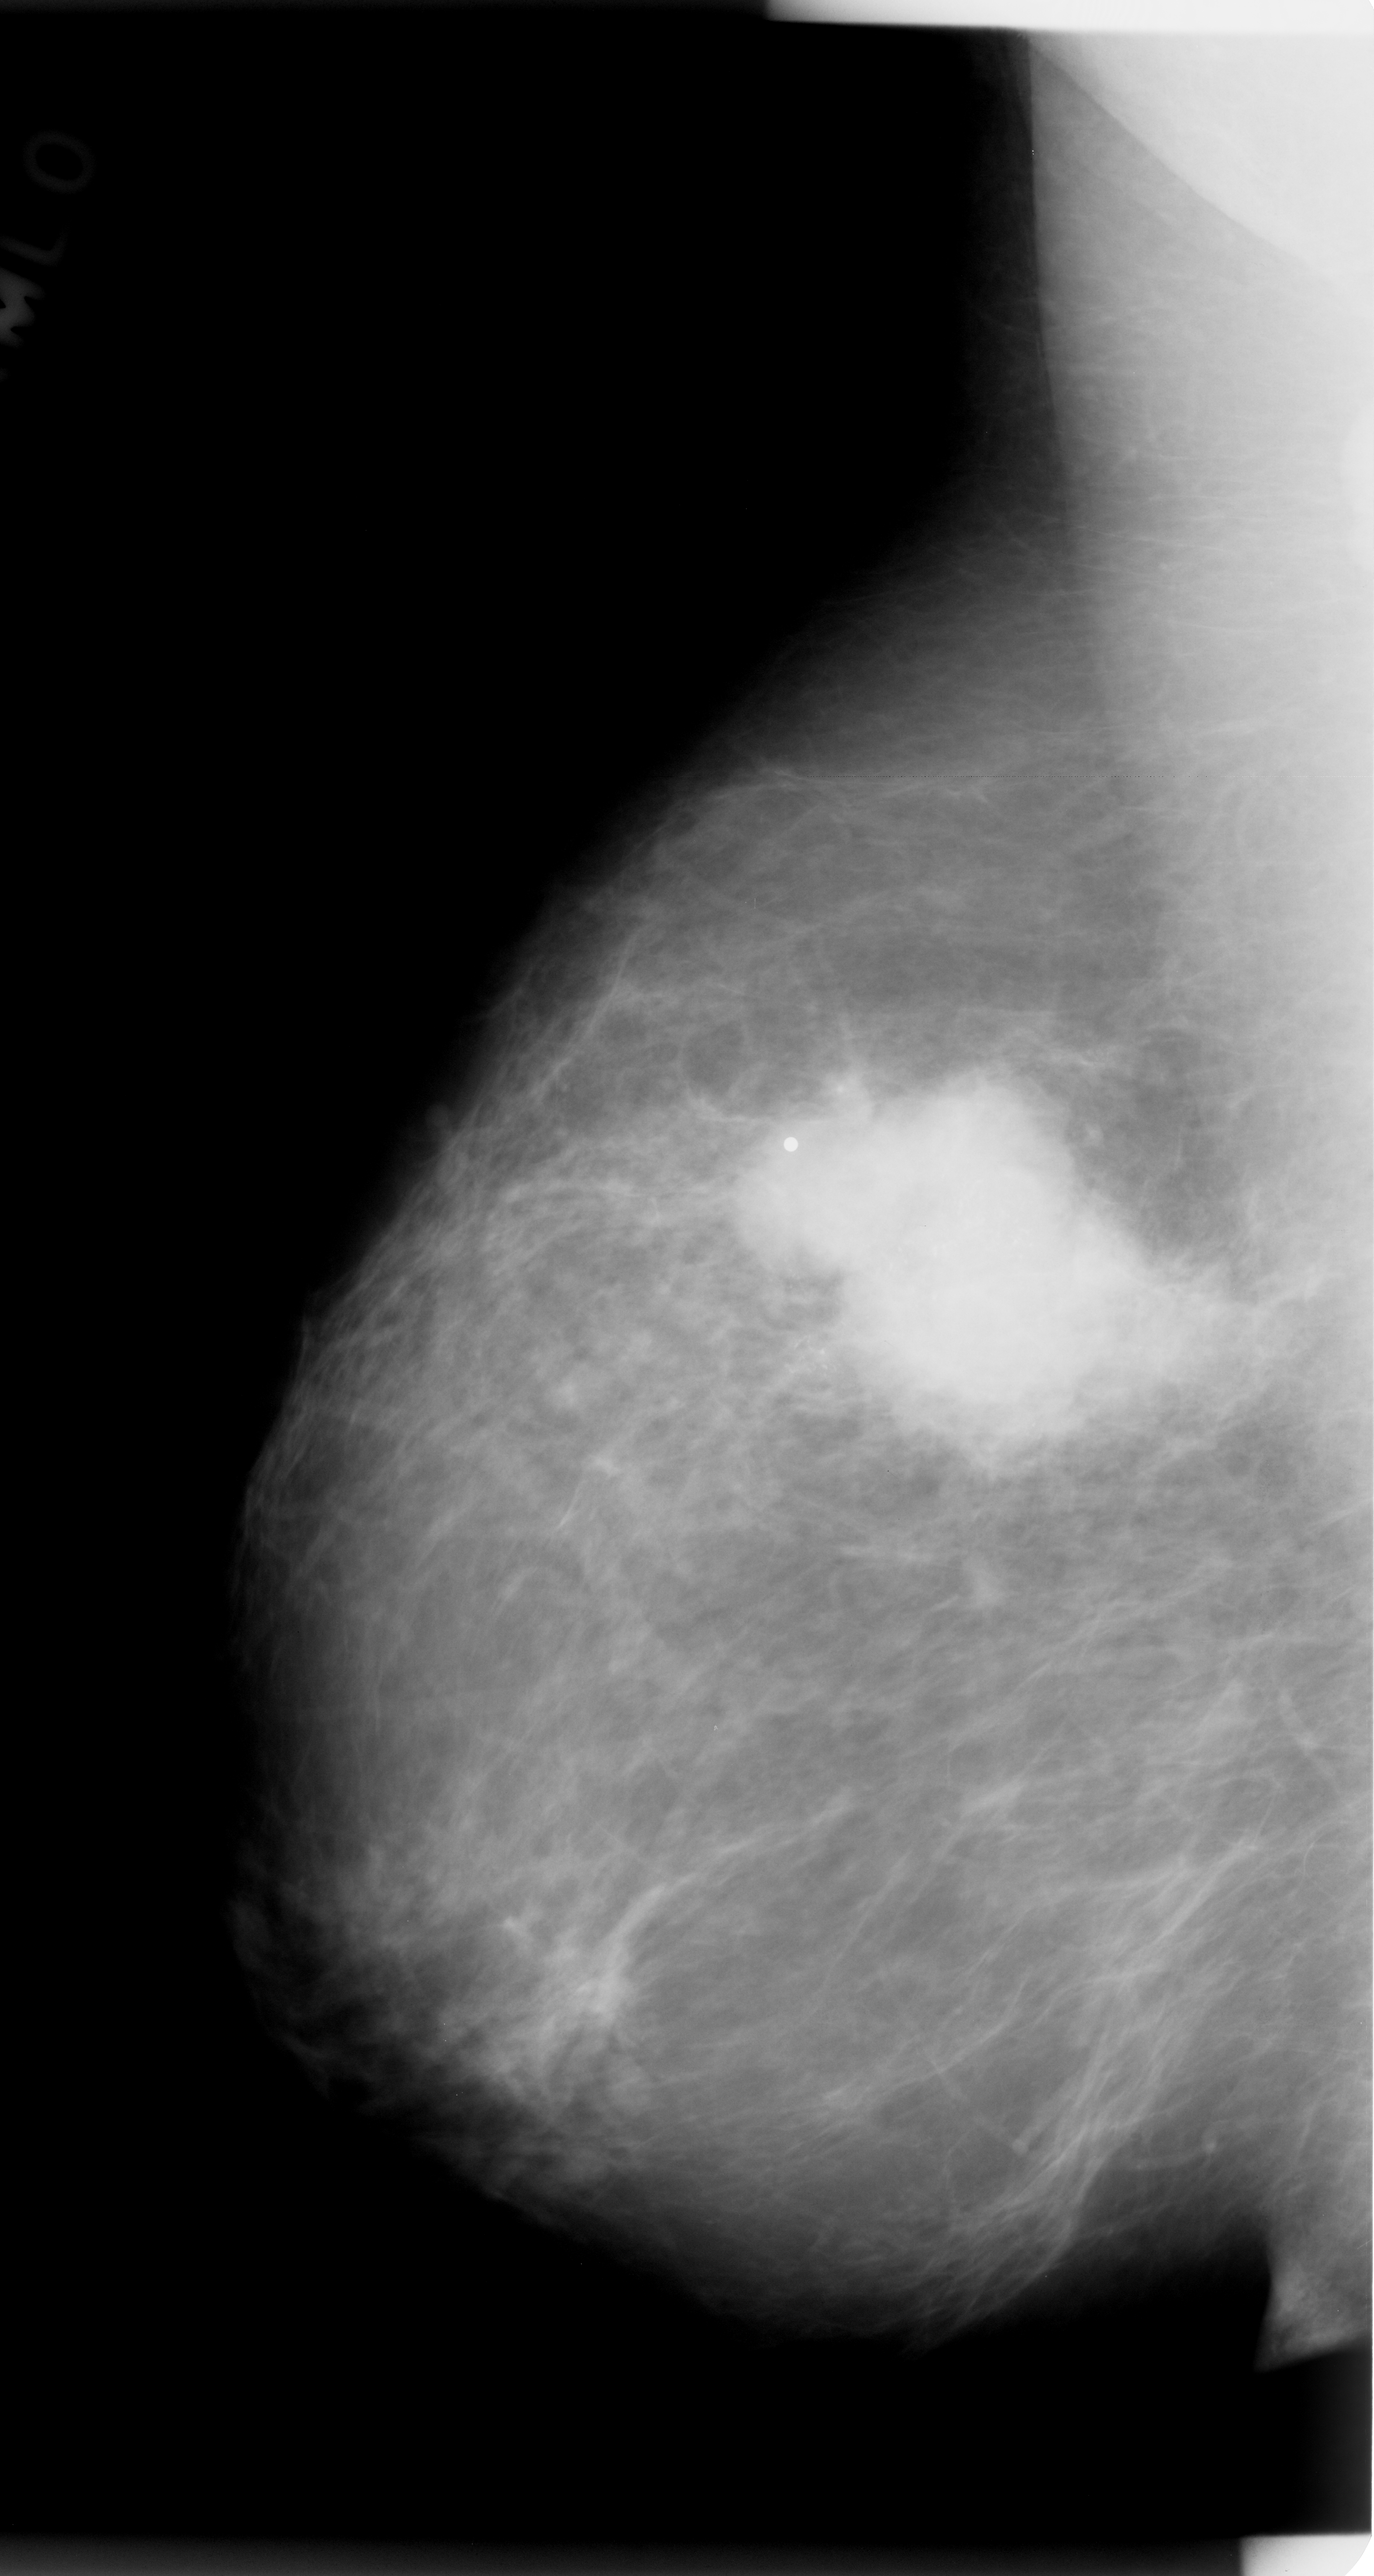
Digitized screen-film mammogram; right breast; MLO view; breast composition: almost entirely fatty (BI-RADS density category 1 of 4).
- Calcifications, morphology pleomorphic, distribution clustered; BI-RADS assessment category 5; subtlety rating 5 on a 1 (subtle) to 5 (obvious) scale; pathology result (as recorded, not read from the image): malignant.